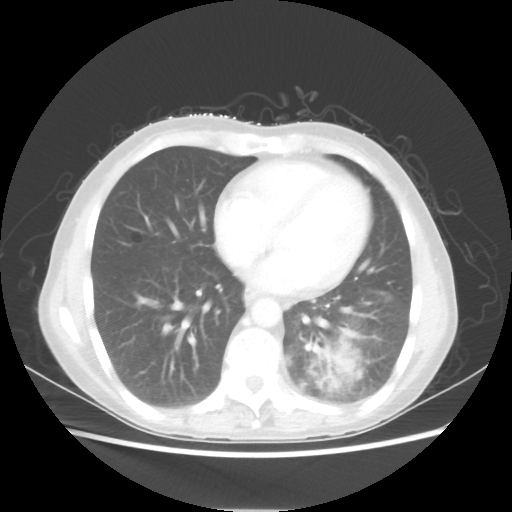
Chest CT, one axial slice. Slice 22 of 56 in the series (ordered by position). Reconstruction kernel STANDARD. 80 kVp. Lung window (W 1500 / L -600 HU). 5 mm slice thickness. 512 × 512 image matrix, field of view 360 × 360 mm. Female patient, age 53 years. Case-level facts recorded for this patient, not image findings: clinical TNM (as recorded): T3 N0 M0.
Outlined on this slice (bounding box drawn by a radiologist):
- lung tumour (recorded histology: adenocarcinoma): bounding box [x1, y1, x2, y2] px = [304, 325, 361, 391]